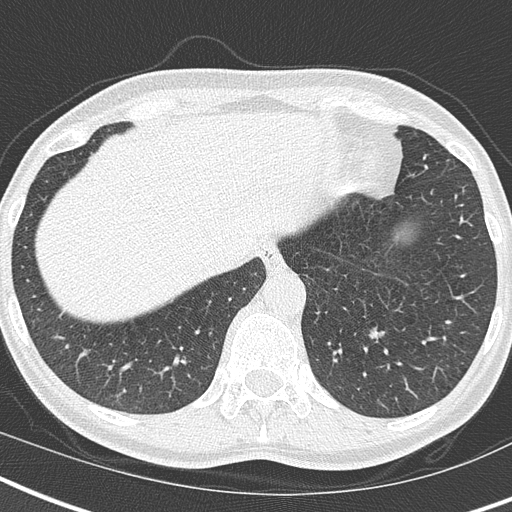
Axial slice from a low-dose chest CT screening exam; third screening round (two years after baseline); lung window (W 1500 / L -600 HU); 2 mm slice thickness; lung (sharp) reconstruction kernel (B50f); slice 130 of 173 in the series; 512 × 512 image matrix, field of view 293 × 293 mm. Female, age 55 years at enrolment. Current smoker at enrolment.
Lesion marked by an expert reader, bounding box [x1, y1, x2, y2] px = [350, 310, 406, 359]. The screening reader recorded 2 non-calcified nodules or masses ≥4 mm on this exam (left lower lobe, right upper lobe); which of them this box marks is not recorded. Lung cancer was diagnosed 349 days after this screen: adenocarcinoma, NOS, left lower lobe, well differentiated (G1), stage IA (AJCC 6th edition), 11 mm at pathology.